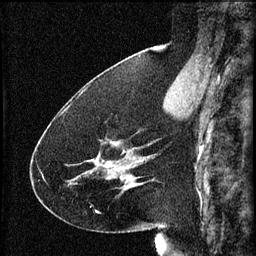
Breast MRI (dynamic contrast-enhanced), one sagittal slice; position 25 of 60 along the scan axis; 3 images stored at this slice position (order not interpretable as contrast timing); 1.5 T; TE 4.2 ms, TR 8.2 ms; 2 mm slice thickness; 256 × 256 image matrix. Patient: female, 41 years.
Structures marked on this image (semi-automatic segmentation, software-assisted and operator-edited):
- analysis volume of interest (the breast-tissue region the enhancement analysis was run in; not a lesion): box from (x=72, y=142) to (x=134, y=193) px
- tumour enhancement mask (voxels above the 70 % enhancement threshold inside the analysis volume of interest): (x=96, y=144)–(x=134, y=189)